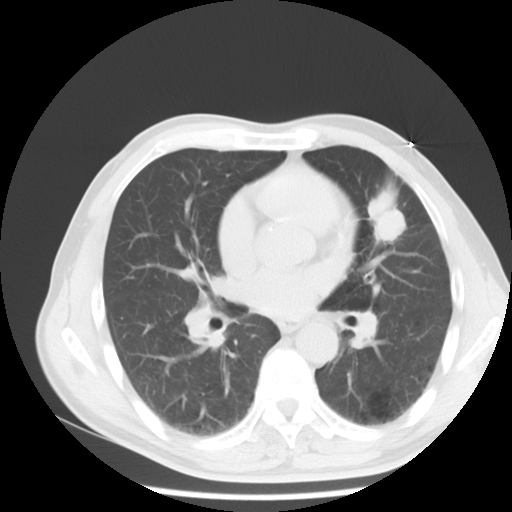
Chest CT, one axial slice. Reconstruction kernel STANDARD. 120 kVp. Lung window (W 1500 / L -600 HU). 512 × 512 image matrix, field of view 350 × 350 mm. Patient: male, 54 years. Case-level facts recorded for this patient, not image findings: clinical TNM (as recorded): T1c N0 M0.
Structures marked on this image (bounding box drawn by a radiologist):
- lung tumour (recorded histology: adenocarcinoma): bounding box <360,190,408,245> (left, top, right, bottom; pixels)